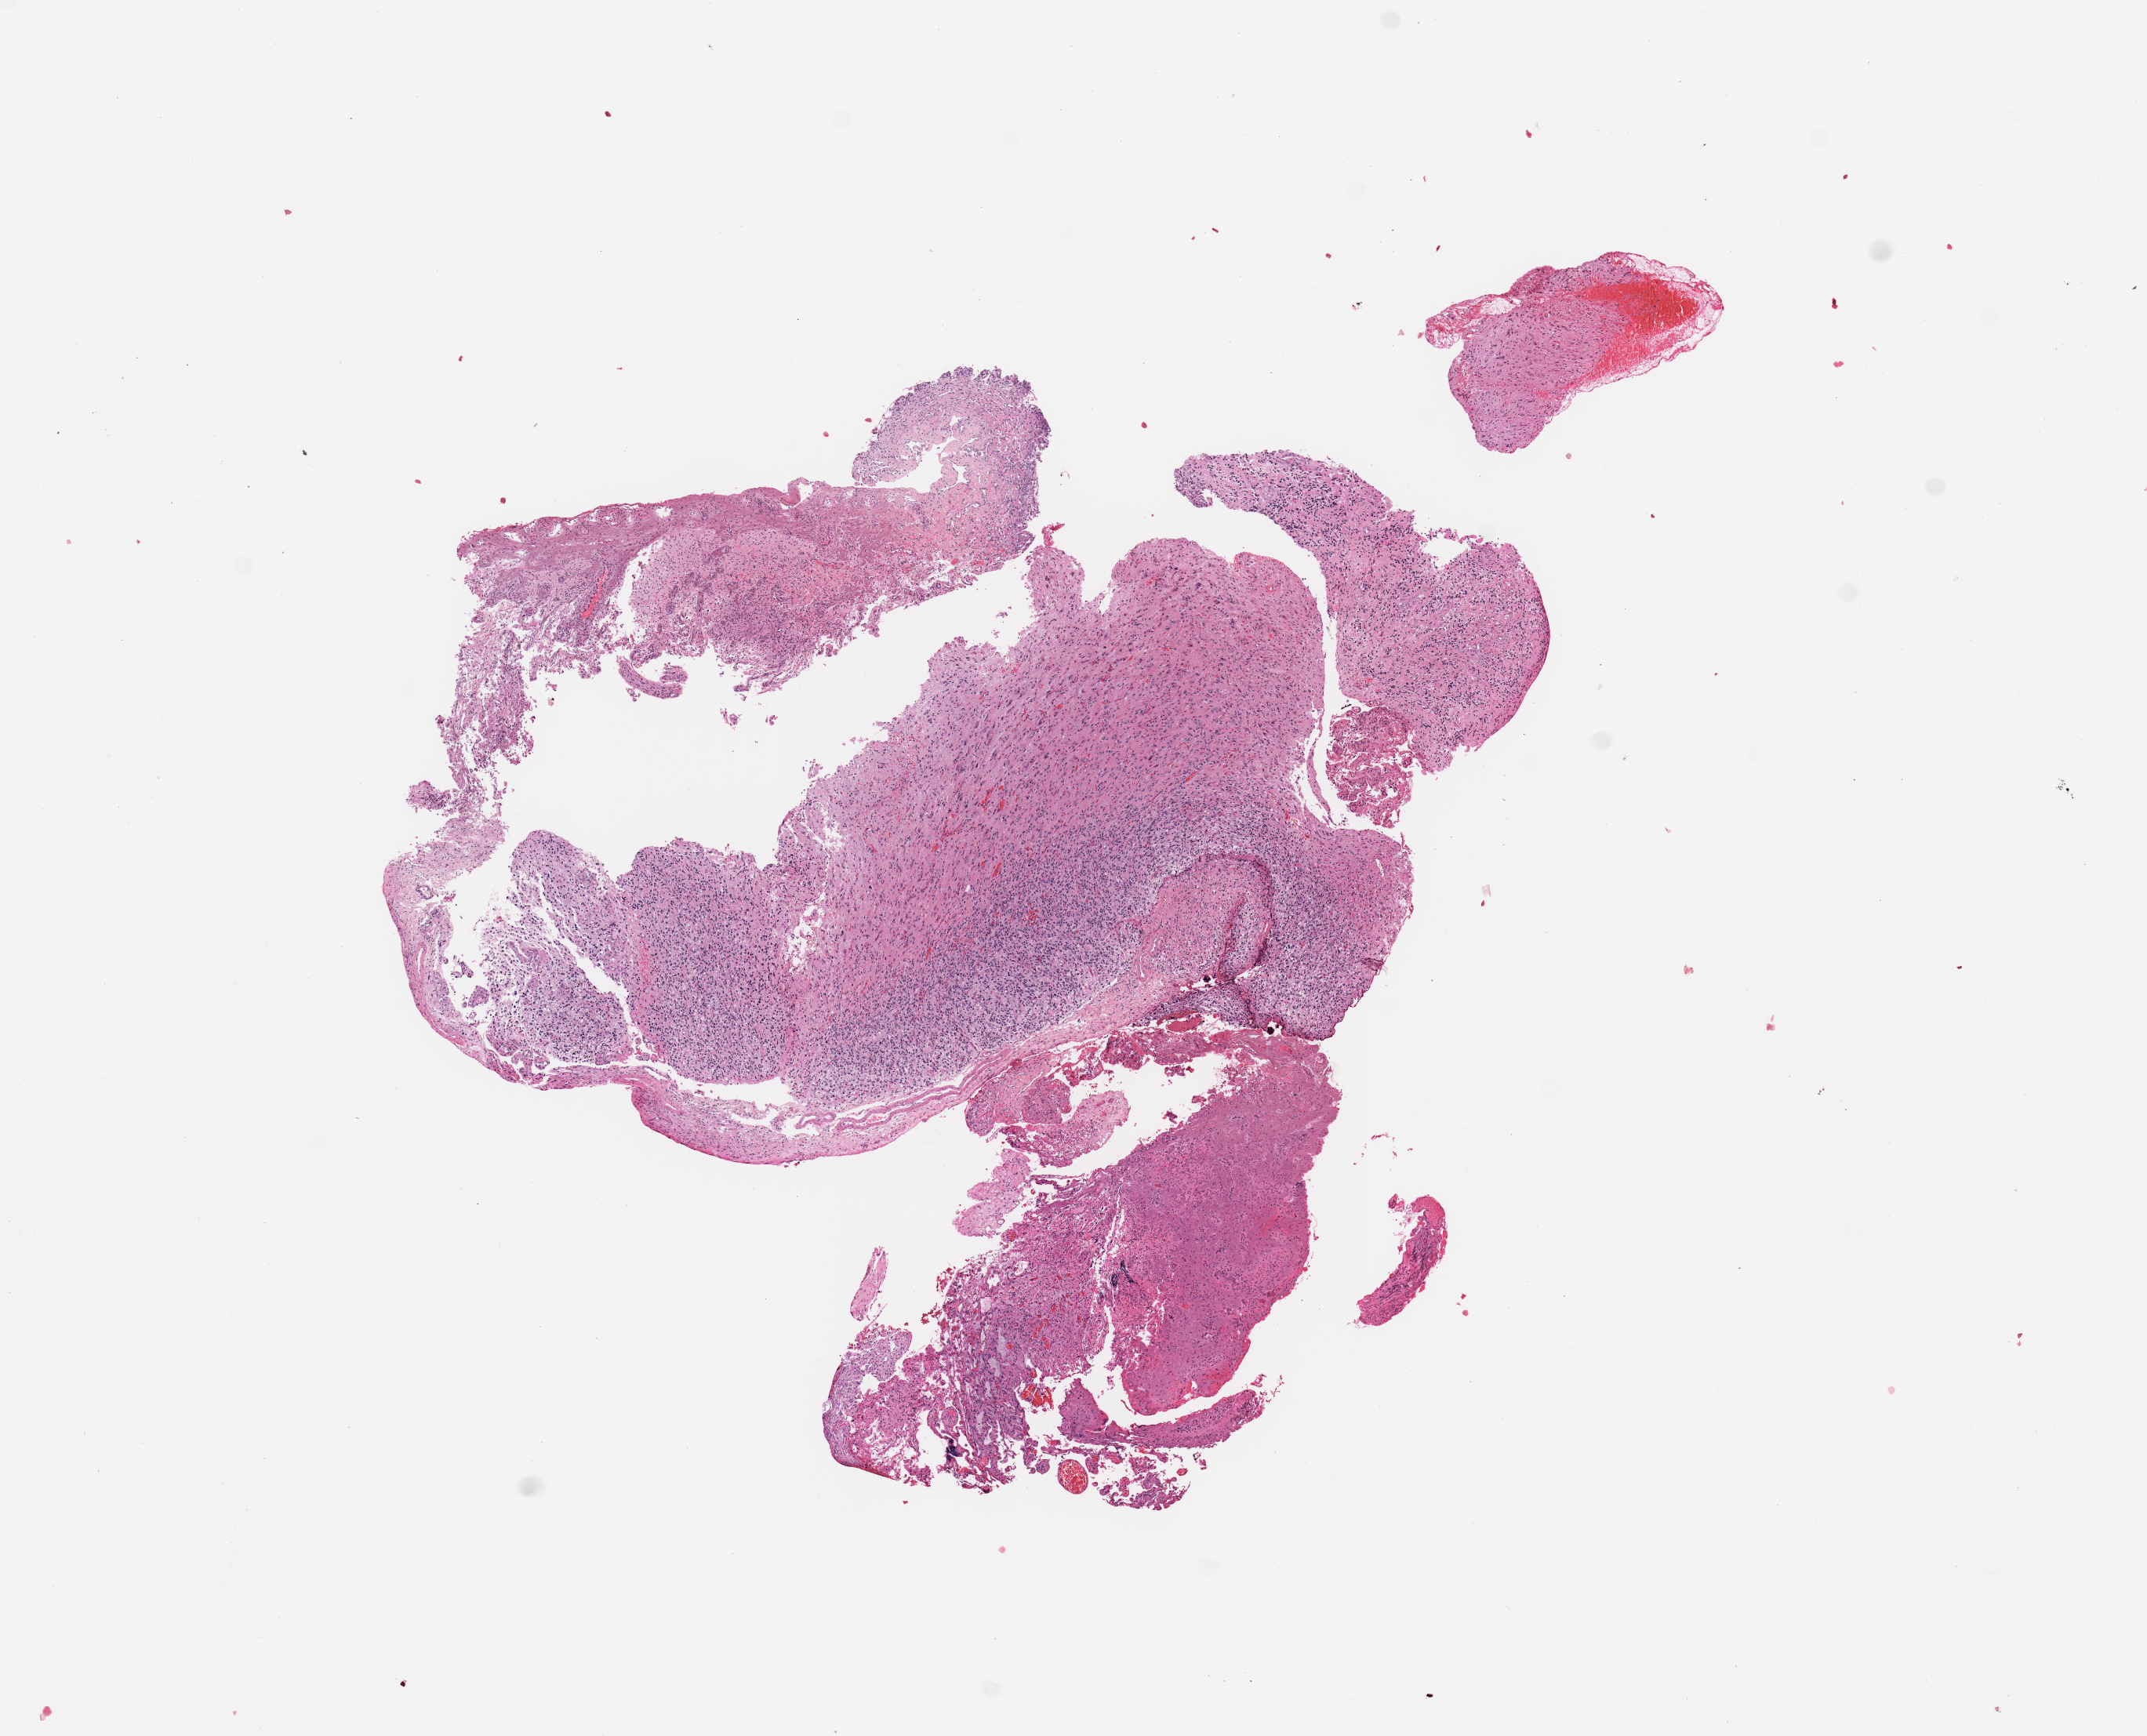
Whole-slide histology image, H&E — a low-resolution overview of the entire scanned area, about 10.8 x 8.8 mm; tumour tissue sample, sampled site: frontal lobe. 77-year-old male patient. Slide review estimates, as recorded: tumour nuclei 60%, necrosis 5%.
Primary tumour site (as recorded): frontal lobe. Histologic diagnosis: Glioblastoma.